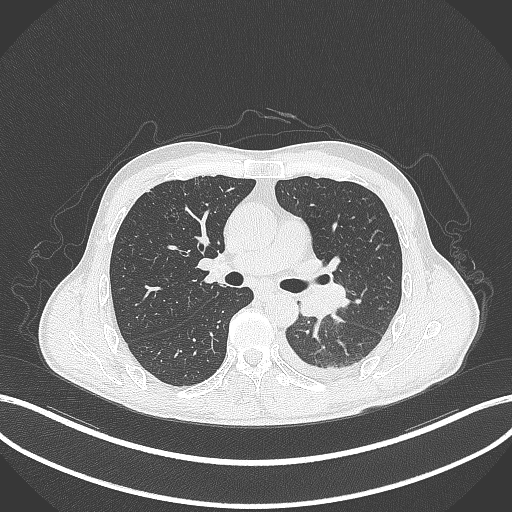
Chest CT, one axial slice. Position 193 of 295 along the scan axis. Lung window (W 1500 / L -600 HU). 1 mm slice thickness. 512 × 512 image matrix, field of view 400 × 400 mm. Male patient, age 47 years. Case-level facts recorded for this patient, not image findings: clinical TNM (as recorded): T3 N1 M1c; histopathological grade: G3.
Structures marked on this image (rectangle marked by the reading radiologist):
- lung tumour (recorded histology: small cell carcinoma): bounding box <295,281,349,319> (left, top, right, bottom; pixels)